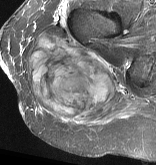
MRI of an extremity soft-tissue mass, one axial slice. Slice 30 of 57 in the series (ordered by position). STIR. MR volume resampled by the dataset authors to the PET/CT grid (not the native acquisition matrix). 3.27 mm slice thickness. 156 × 165 image matrix. Female patient. From the clinical record (not read from this slice): histological type: epithelioid sarcoma with vascular differentiation; site of the primary tumour: right buttock.
Structures marked on this image (expert contour drawn on MRI and transferred to this co-registered scan by the dataset authors):
- gross tumour volume (mass): bounding box <26,32,116,118> (left, top, right, bottom; pixels)